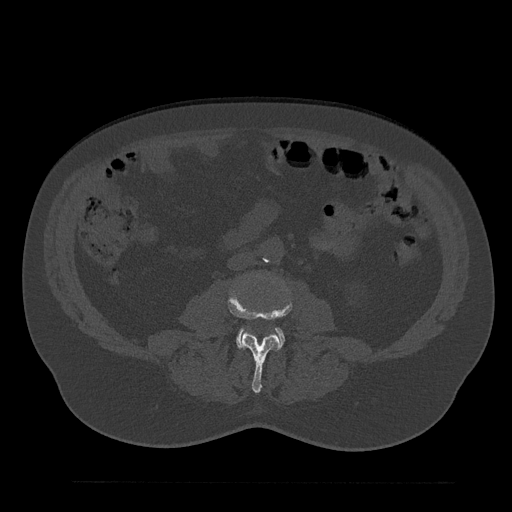
CT including the spine, one axial slice; slice 9 of 797 in the series (ordered by position); reconstruction kernel Br40s/3; bone window (W 1800 / L 400 HU); 0.5 mm slice thickness; 512 × 512 image matrix, field of view 430 × 430 mm. Patient: male, 61 years. Case-level facts recorded for this patient, not image findings: primary cancer: prostate.
Annotated regions visible in this slice (semi-automatic segmentation, software-assisted and operator-edited):
- L3 vertebra: bounding box <228,275,292,393> (left, top, right, bottom; pixels)
- L4 vertebra: <236,328,284,346>